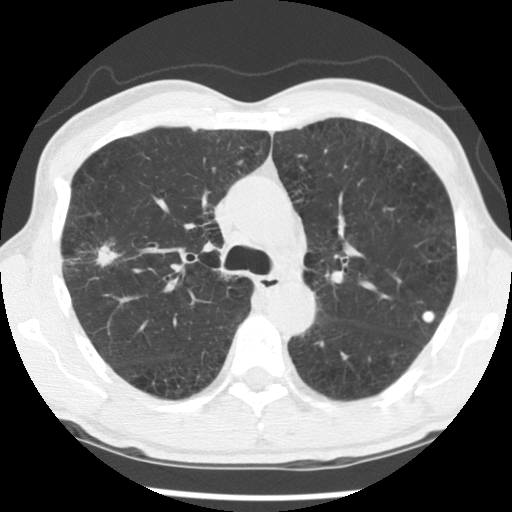
Low-dose screening chest CT, axial slice; second annual screen; lung window (W 1500 / L -600 HU); 2.5 mm slice thickness; standard (soft-tissue) reconstruction kernel (STANDARD); slice 87 of 138 in the series; 512 × 512 image matrix, field of view 320 × 320 mm. Male participant, aged 56 years at enrolment. Current smoker at enrolment.
Expert-annotated lung lesion, box from (x=52, y=232) to (x=138, y=292) px. Reader record for this screening exam (exam-level; its link to the box is not recorded): non-calcified nodule or mass ≥4 mm, right upper lobe, 30 × 18 mm, spiculated (stellate) margins, mixed attenuation, pre-existing on the prior screen: yes; interval growth: yes. Official screen result: positive, other. Later outcome: lung cancer diagnosed 326 days after this screen — squamous cell carcinoma, NOS, right upper lobe, right middle lobe, moderately differentiated (G2), stage IB (AJCC 6th edition), 70 mm at pathology.